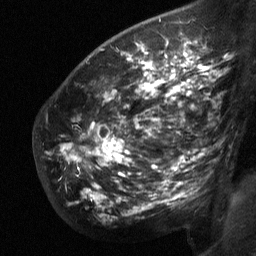
Breast MRI (dynamic contrast-enhanced), one sagittal slice; position 43 of 64 along the scan axis; dynamic contrast-enhanced study with each time point stored as its own series, time point 2 of 3 at this slice position (early post-contrast, ordered by acquisition time); 1.5 T; TE 4.8 ms, TR 27 ms; 2 mm slice thickness; 256 × 256 image matrix, field of view 200 × 200 mm. Female patient, age 50 years. Case-level facts recorded for this patient, not image findings: setting: breast cancer imaged before/during neoadjuvant chemotherapy; receptor status: HER2-positive.
Structures marked on this image (semi-automatic segmentation, software-assisted and operator-edited):
- analysis volume of interest (the breast-tissue region the enhancement analysis was run in; not a lesion): bounding box (x1, y1, x2, y2) in pixels: (49, 62, 212, 205)
- tumour enhancement mask (voxels above the 90 % enhancement threshold inside the analysis volume of interest): (89, 62, 202, 169)